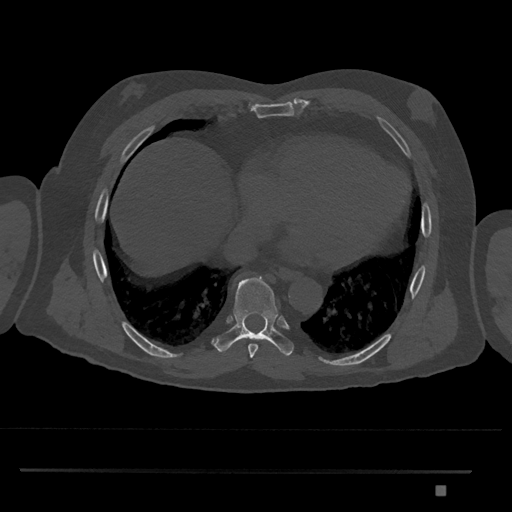
CT including the spine, one axial slice; slice 1123 of 1134 in the series (ordered by position); reconstruction kernel Br40s/3; 120 kVp; bone window (W 1800 / L 400 HU); 0.5 mm slice thickness; 512 × 512 image matrix, field of view 429 × 429 mm. Patient: male, 65 years. Case-level facts recorded for this patient, not image findings: primary cancer: prostate.
Structures marked on this image (semi-automatically segmented with operator editing):
- T8 vertebra: bounding box [x1, y1, x2, y2] px = [214, 276, 294, 357]